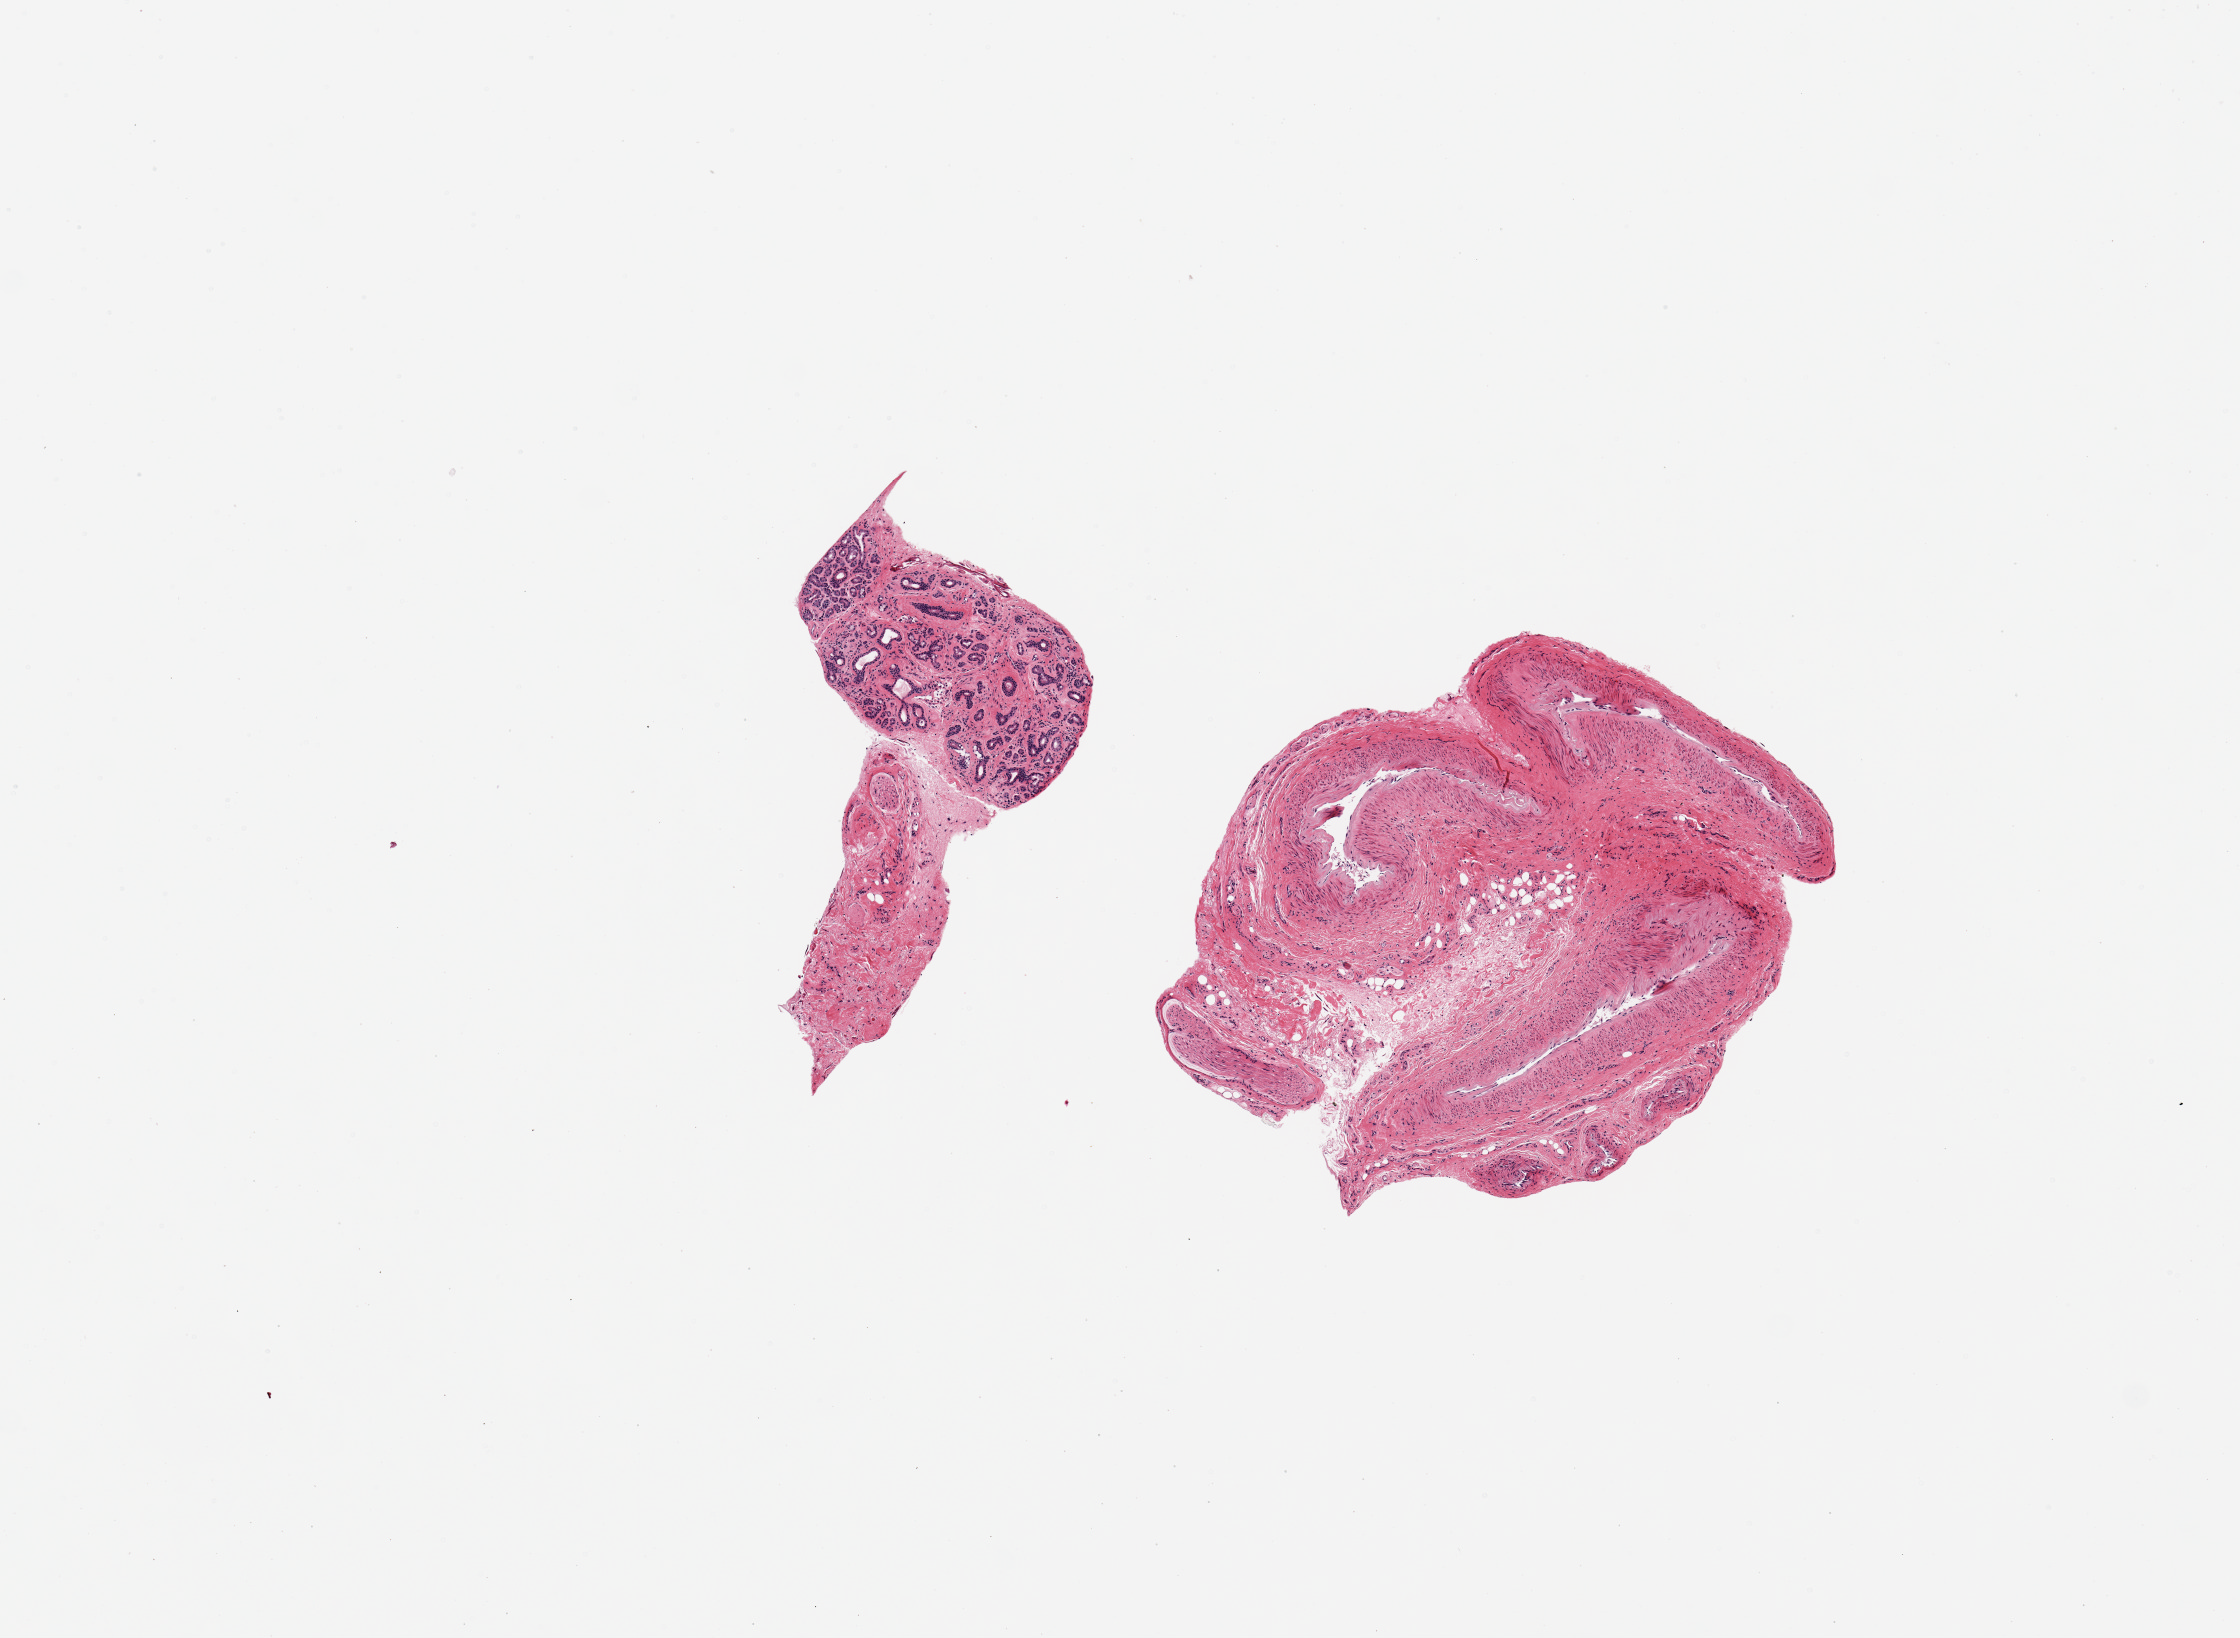
Whole-slide image, haematoxylin and eosin stain, shown as a low-resolution overview of the whole scanned area (about 8.9 x 6.5 mm), PAXgene-fixed, paraffin-embedded tissue, target tissue: minor salivary gland, tissue donor sample. Male donor.
• reviewer comment on this tissue sample: 2 pieces; rest is fibrous/connective/vascular tissue, avoid